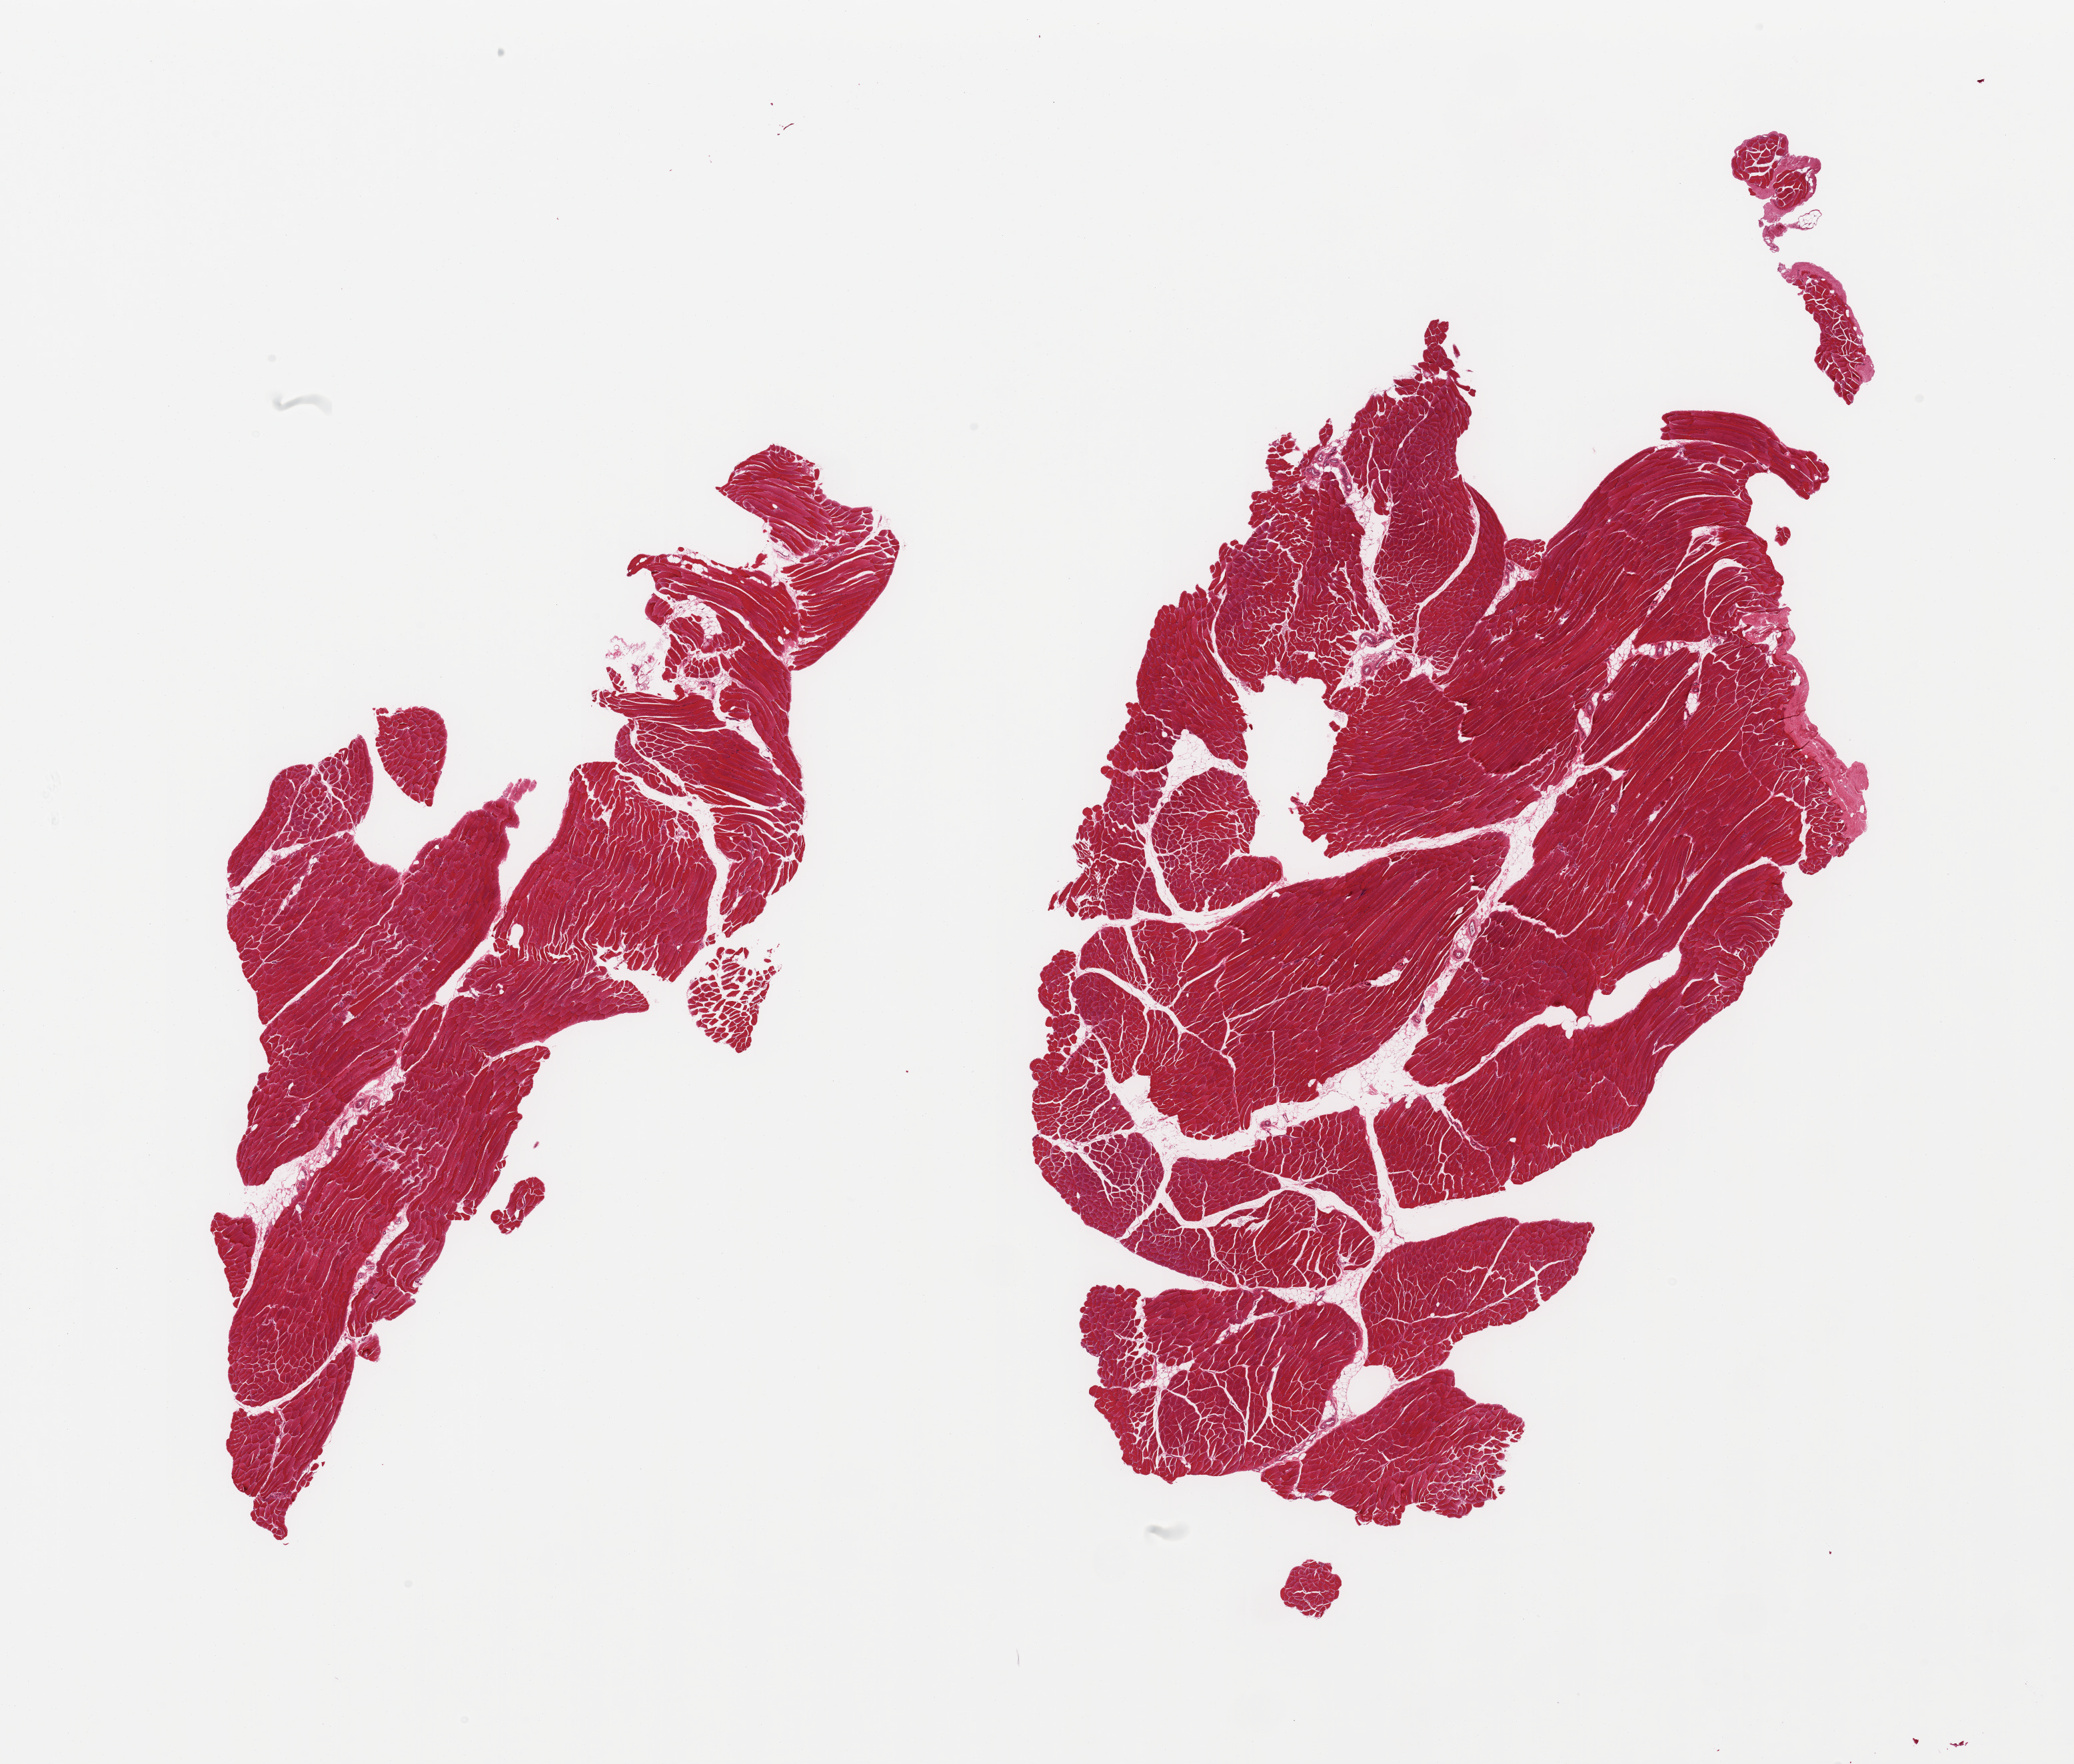
Digitized haematoxylin and eosin-stained section — a low-resolution overview of the entire scanned area, about 24.6 x 20.9 mm (acquisition: 20x scan), PAXgene-fixed, paraffin-embedded tissue, section of skeletal muscle (target tissue), donor tissue sample.
• pathologist's review note for this sample: 2 slightly fragmented pieces: 5% internal fat